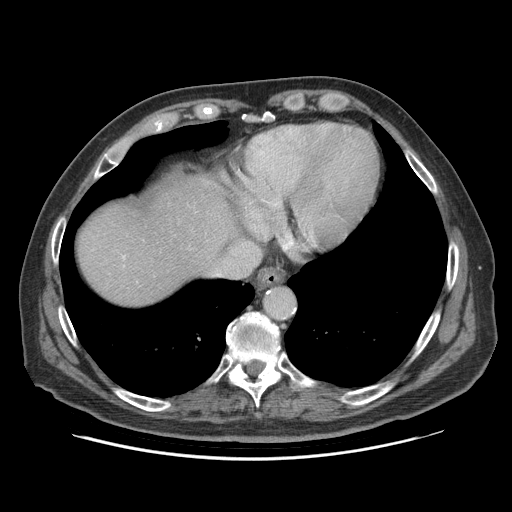
Contrast-enhanced abdominal CT (liver protocol), one axial slice; slice 80 of 95 in the series (ordered by position); soft-tissue window (W 400 / L 40 HU); 2.5 mm slice thickness; 512 × 512 image matrix, field of view 400 × 400 mm. From the clinical record (not read from this slice): diagnosis: hepatocellular carcinoma (patient treated with transarterial chemoembolisation; whether this scan precedes or follows treatment is not stated here); TNM stage (as recorded): Stage-IVB; Child-Pugh class: A; tumour nodularity: uninodular.
Structures marked on this image (semi-automatic segmentation, software-assisted and operator-edited):
- liver parenchyma outside the tumour (the mass and vessels are separate outlines, so this box may not span the whole liver): bounding box <78,174,236,306> (left, top, right, bottom; pixels)